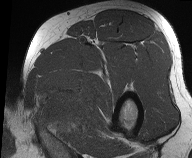
MRI of an extremity soft-tissue mass, one axial slice; position 44 of 61 along the scan axis; MR volume resampled by the dataset authors to the PET/CT grid (not the native acquisition matrix); 3.27 mm slice thickness; 192 × 158 image matrix, field of view 187 × 154 mm. Male patient. Case-level facts recorded for this patient, not image findings: histological type: pleiomorphic liposarcoma; grade: high; site of the primary tumour: left thigh.
Outlined on this slice (expert contour drawn on MRI and transferred to this co-registered scan by the dataset authors):
- gross tumour volume including surrounding oedema: bounding box <32,78,87,129> (left, top, right, bottom; pixels)